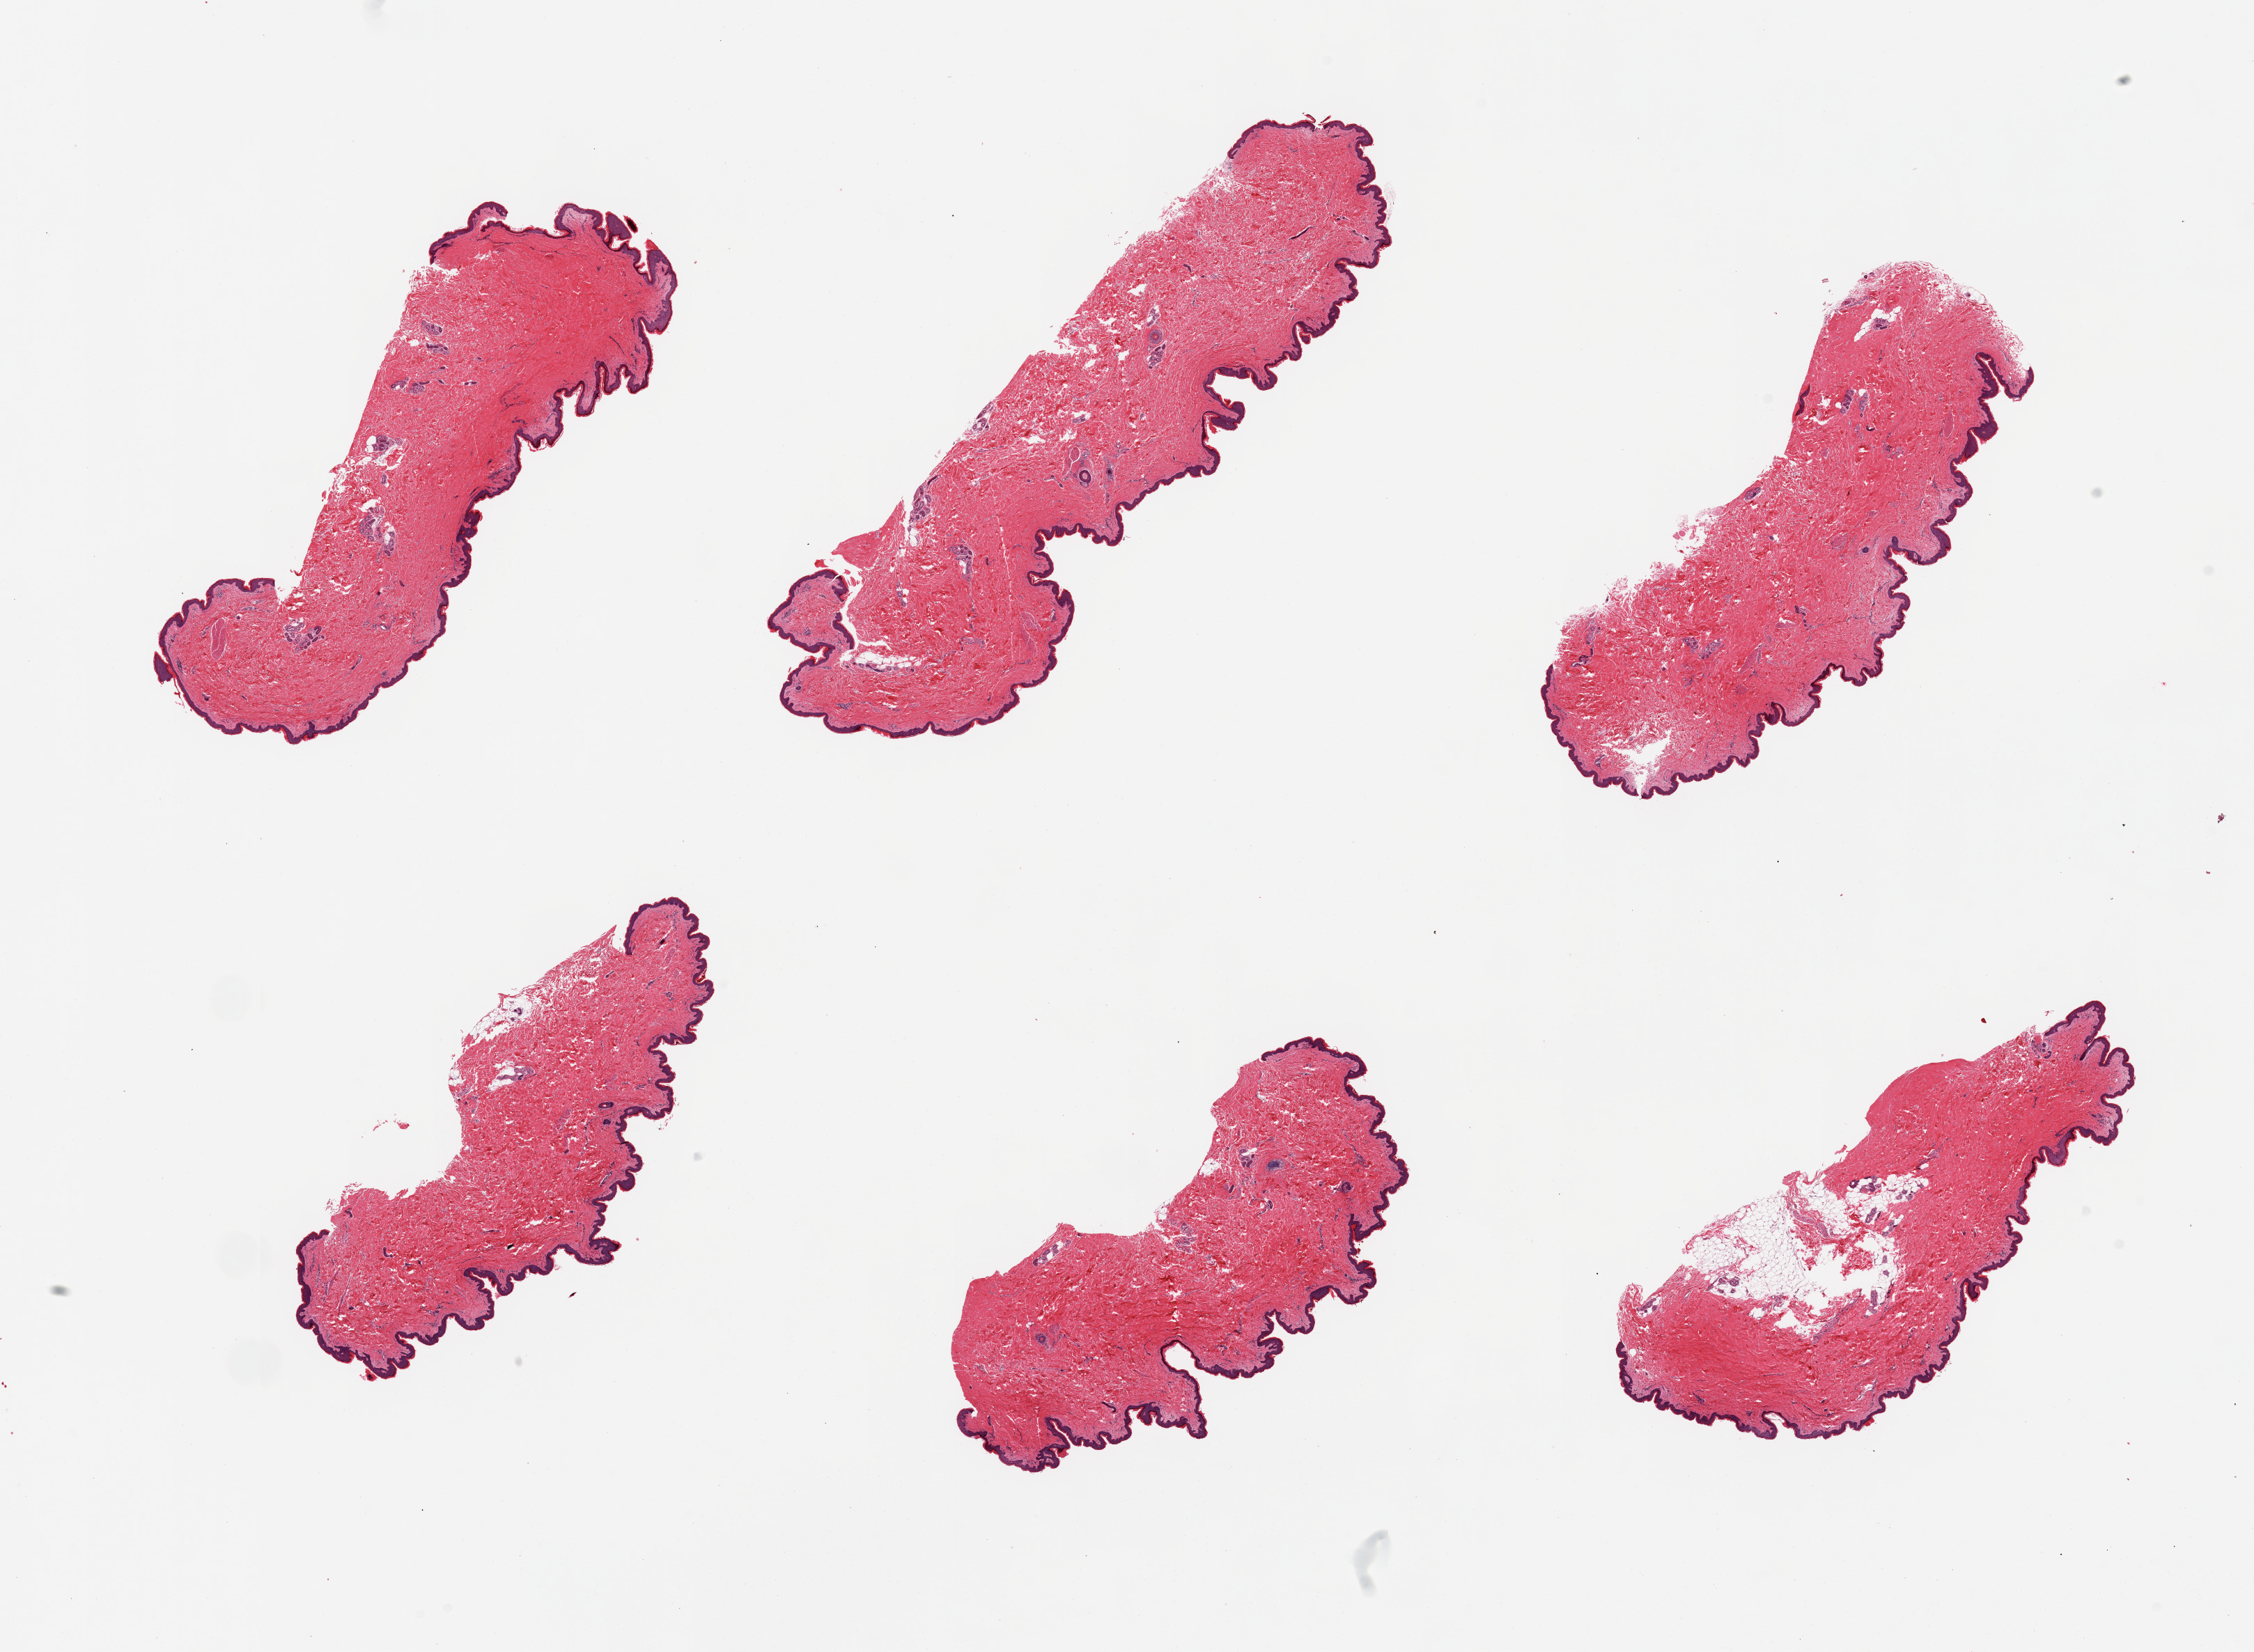
Digitized haematoxylin and eosin-stained section, brightfield — shown as a low-resolution overview of the whole scanned area (about 25.6 x 18.8 mm, from a 20x scan); PAXgene-fixed, paraffin-embedded tissue; section of skin of suprapubic region (target tissue); donor tissue sample. Donor: male.
Review note (as recorded): 6 pieces; well trimmed, but 1 includes 20% fat.